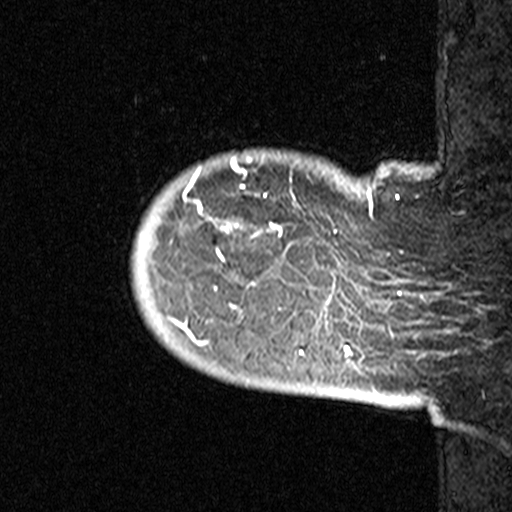
Breast MRI (dynamic contrast-enhanced), one sagittal slice; slice 4 of 44 in the series (ordered by position); dynamic contrast-enhanced study with each time point stored as its own series, time point 2 of 3 at this slice position (early post-contrast, ordered by acquisition time); 1.5 T; TE 4.5 ms, TR 11 ms; 3 mm slice thickness; 512 × 512 image matrix, field of view 200 × 200 mm. Female patient, age 53 years. From the clinical record (not read from this slice): setting: breast cancer imaged before/during neoadjuvant chemotherapy; receptor status: HR-positive, HER2-negative.
Structures marked on this image (semi-automatic segmentation, software-assisted and operator-edited):
- analysis volume of interest (the breast-tissue region the enhancement analysis was run in; not a lesion): bounding box <130,147,311,353> (left, top, right, bottom; pixels)
- tumour enhancement mask (voxels above the 90 % enhancement threshold inside the analysis volume of interest): <173,160,303,353>